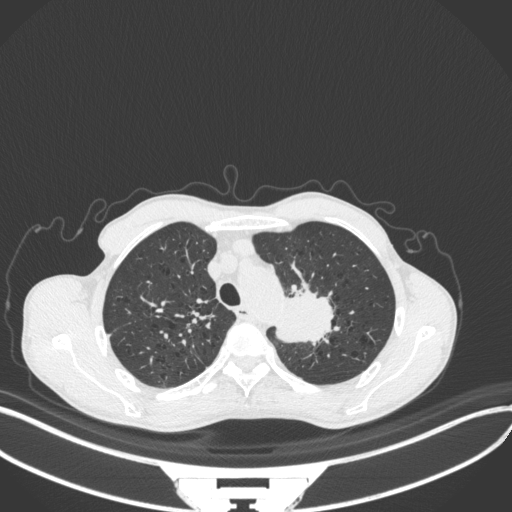
Chest CT, one axial slice; slice 334 of 394 in the series (ordered by position); 120 kVp; lung window (W 1500 / L -600 HU); 512 × 512 image matrix, field of view 400 × 400 mm. Patient: male, 65 years. From the clinical record (not read from this slice): clinical TNM (as recorded): T2b N0 M0.
Annotated regions visible in this slice (rectangle marked by the reading radiologist):
- lung tumour (recorded histology: adenocarcinoma): box from (x=272, y=273) to (x=337, y=348) px